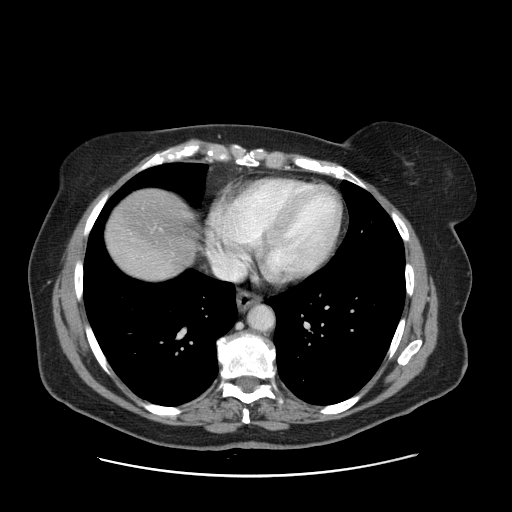
Contrast-enhanced abdominal CT, one axial slice; 120 kVp; intravenous contrast given; soft-tissue window (W 400 / L 40 HU); 2.5 mm slice thickness; 512 × 512 image matrix, field of view 398 × 398 mm. Female patient, age 62 years. From the clinical record (not read from this slice): diagnosis: colorectal cancer liver metastases, imaged before liver resection; multiple liver metastases: no; largest metastasis: 2.5 cm; chemotherapy before resection: yes.
Outlined on this slice (expert manual segmentation):
- liver: bounding box (x1, y1, x2, y2) in pixels: (107, 190, 198, 278)
- planned liver remnant (the part of the liver to remain after resection): (107, 190, 197, 269)